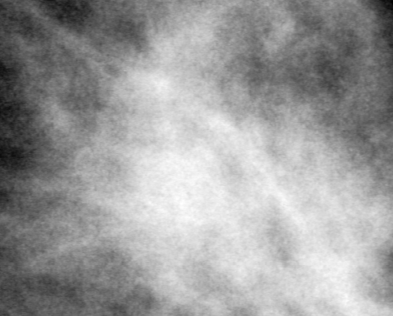
Region of interest cut from a scanned film mammogram (one marked finding), right breast, MLO view, BI-RADS breast density category 3 (scale 1–4).
Finding: calcifications, morphology pleomorphic, distribution linear; BI-RADS assessment category 4; pathology (as recorded): benign.